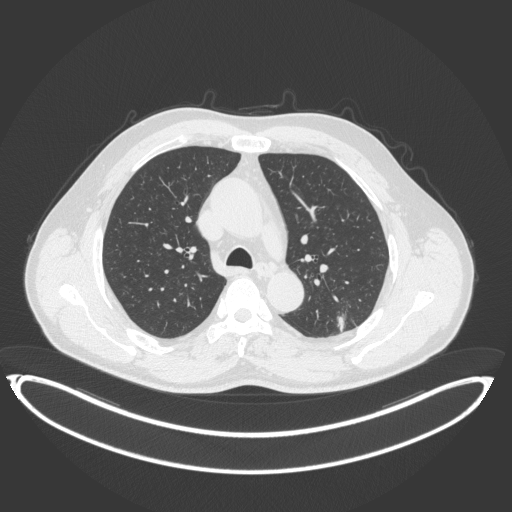
Chest CT, one axial slice. Position 242 of 399 along the scan axis. 120 kVp. Lung window (W 1500 / L -600 HU). 1 mm slice thickness. 512 × 512 image matrix, field of view 469 × 469 mm. Patient: male, 58 years. From the clinical record (not read from this slice): clinical TNM (as recorded): T1c N0 M0; histopathological grade: G1-2.
Outlined on this slice (bounding box drawn by a radiologist):
- lung tumour (recorded histology: adenocarcinoma): bounding box (x1, y1, x2, y2) in pixels: (330, 296, 357, 332)